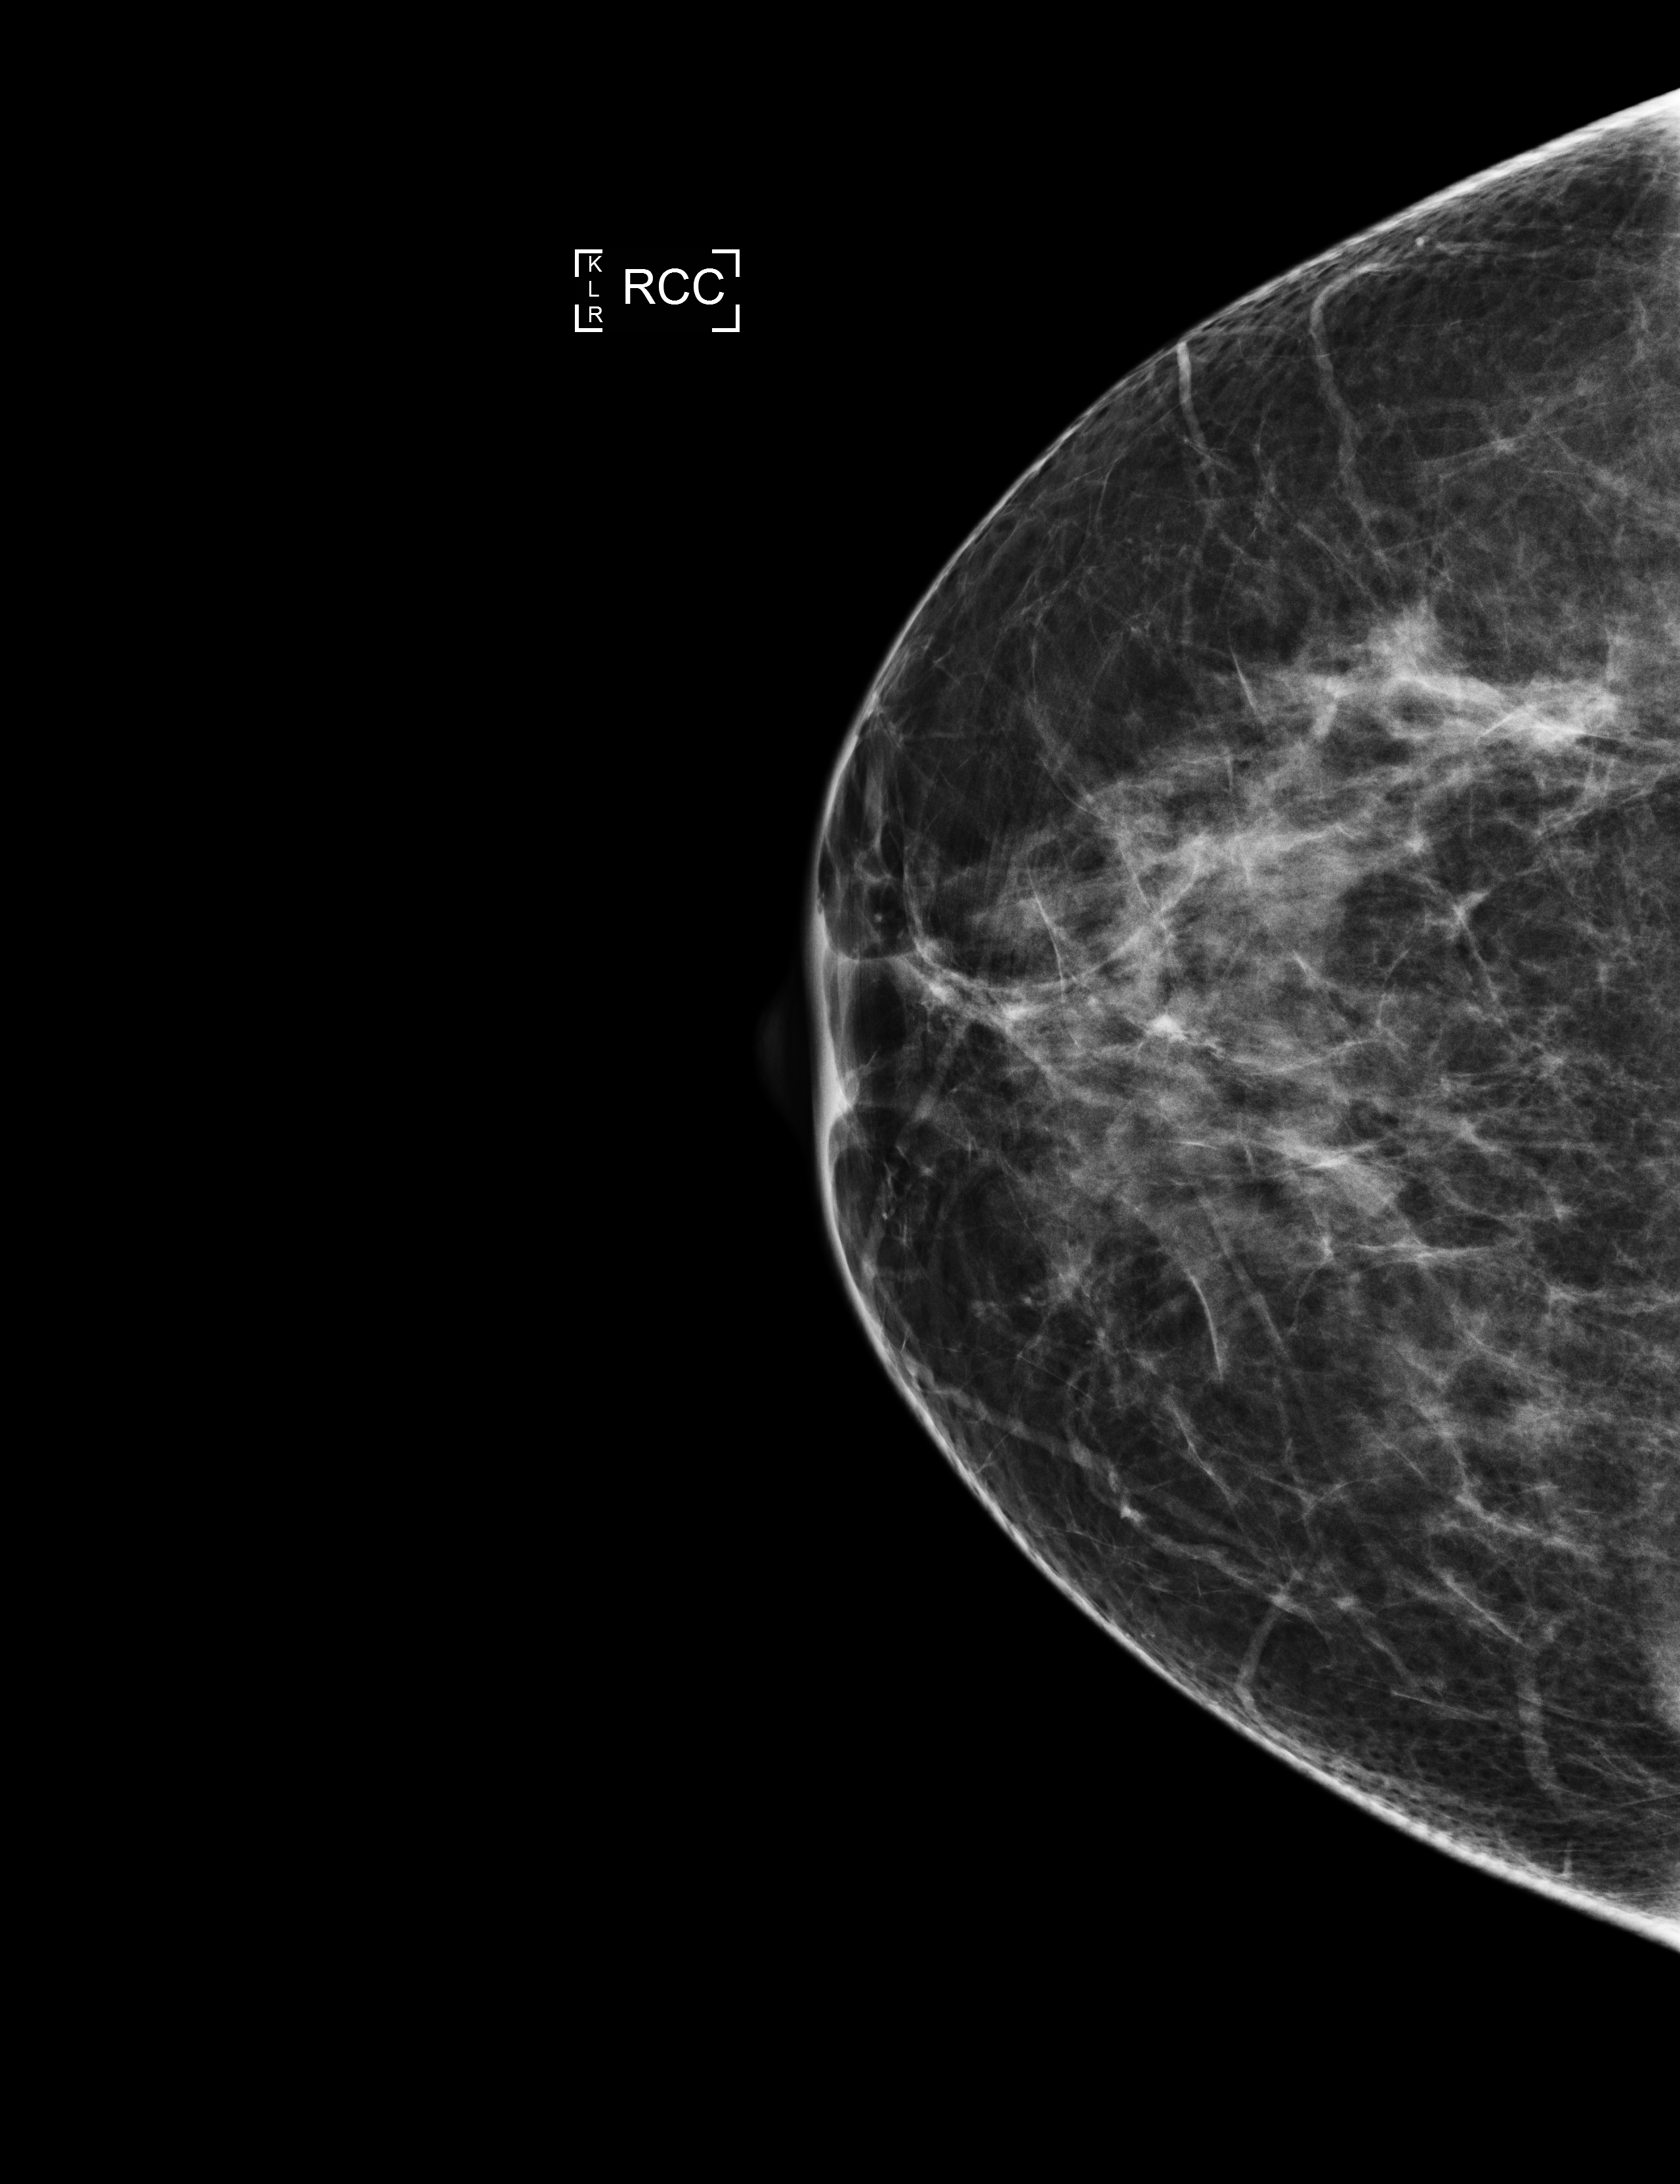
Annual screening mammography examination; compressed breast thickness 68 mm. Patient aged 47 years (female).
Image type: full-field digital mammogram. Breast: right. Projection: cranio-caudal projection.